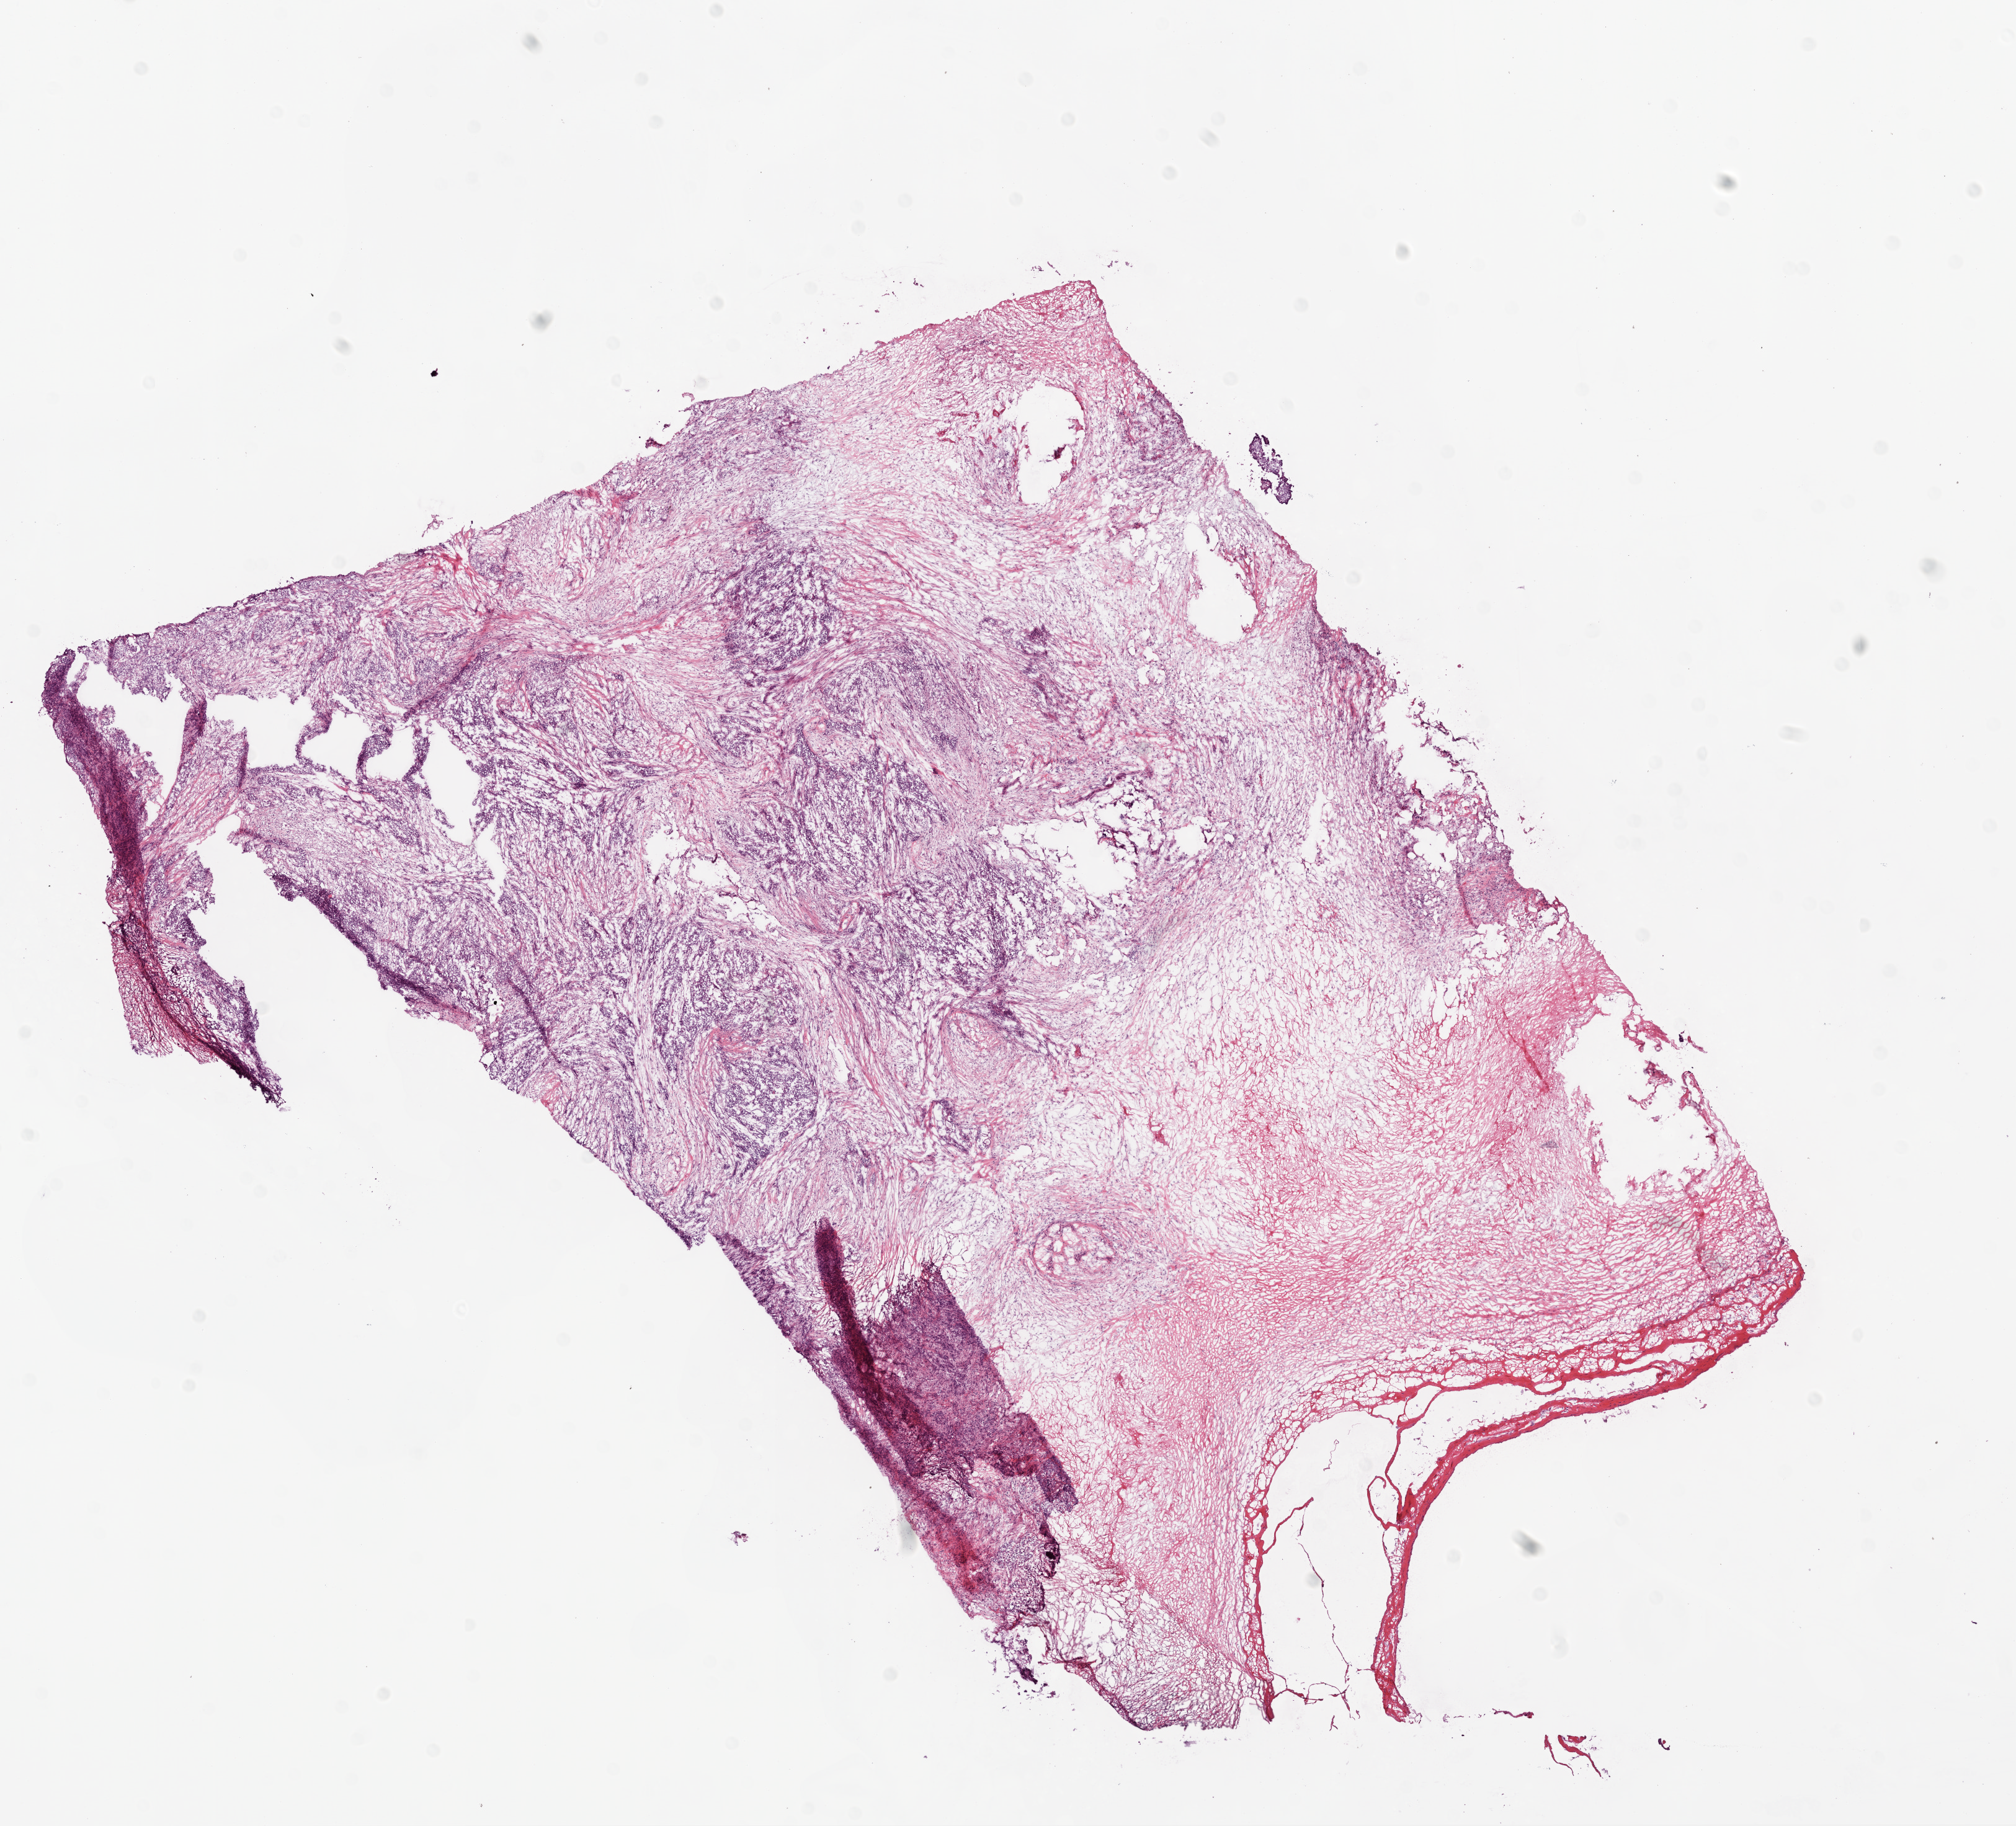
H&E whole-slide image — low-resolution overview of the scanned area, about 13.0 x 11.8 mm (slide scanned at 20x). Frozen section from the bottom of the tissue portion. Primary tumour sample from the ovary. Female patient; age at initial diagnosis 50 years.
Pathologic diagnosis: Serous cystadenocarcinoma, NOS.